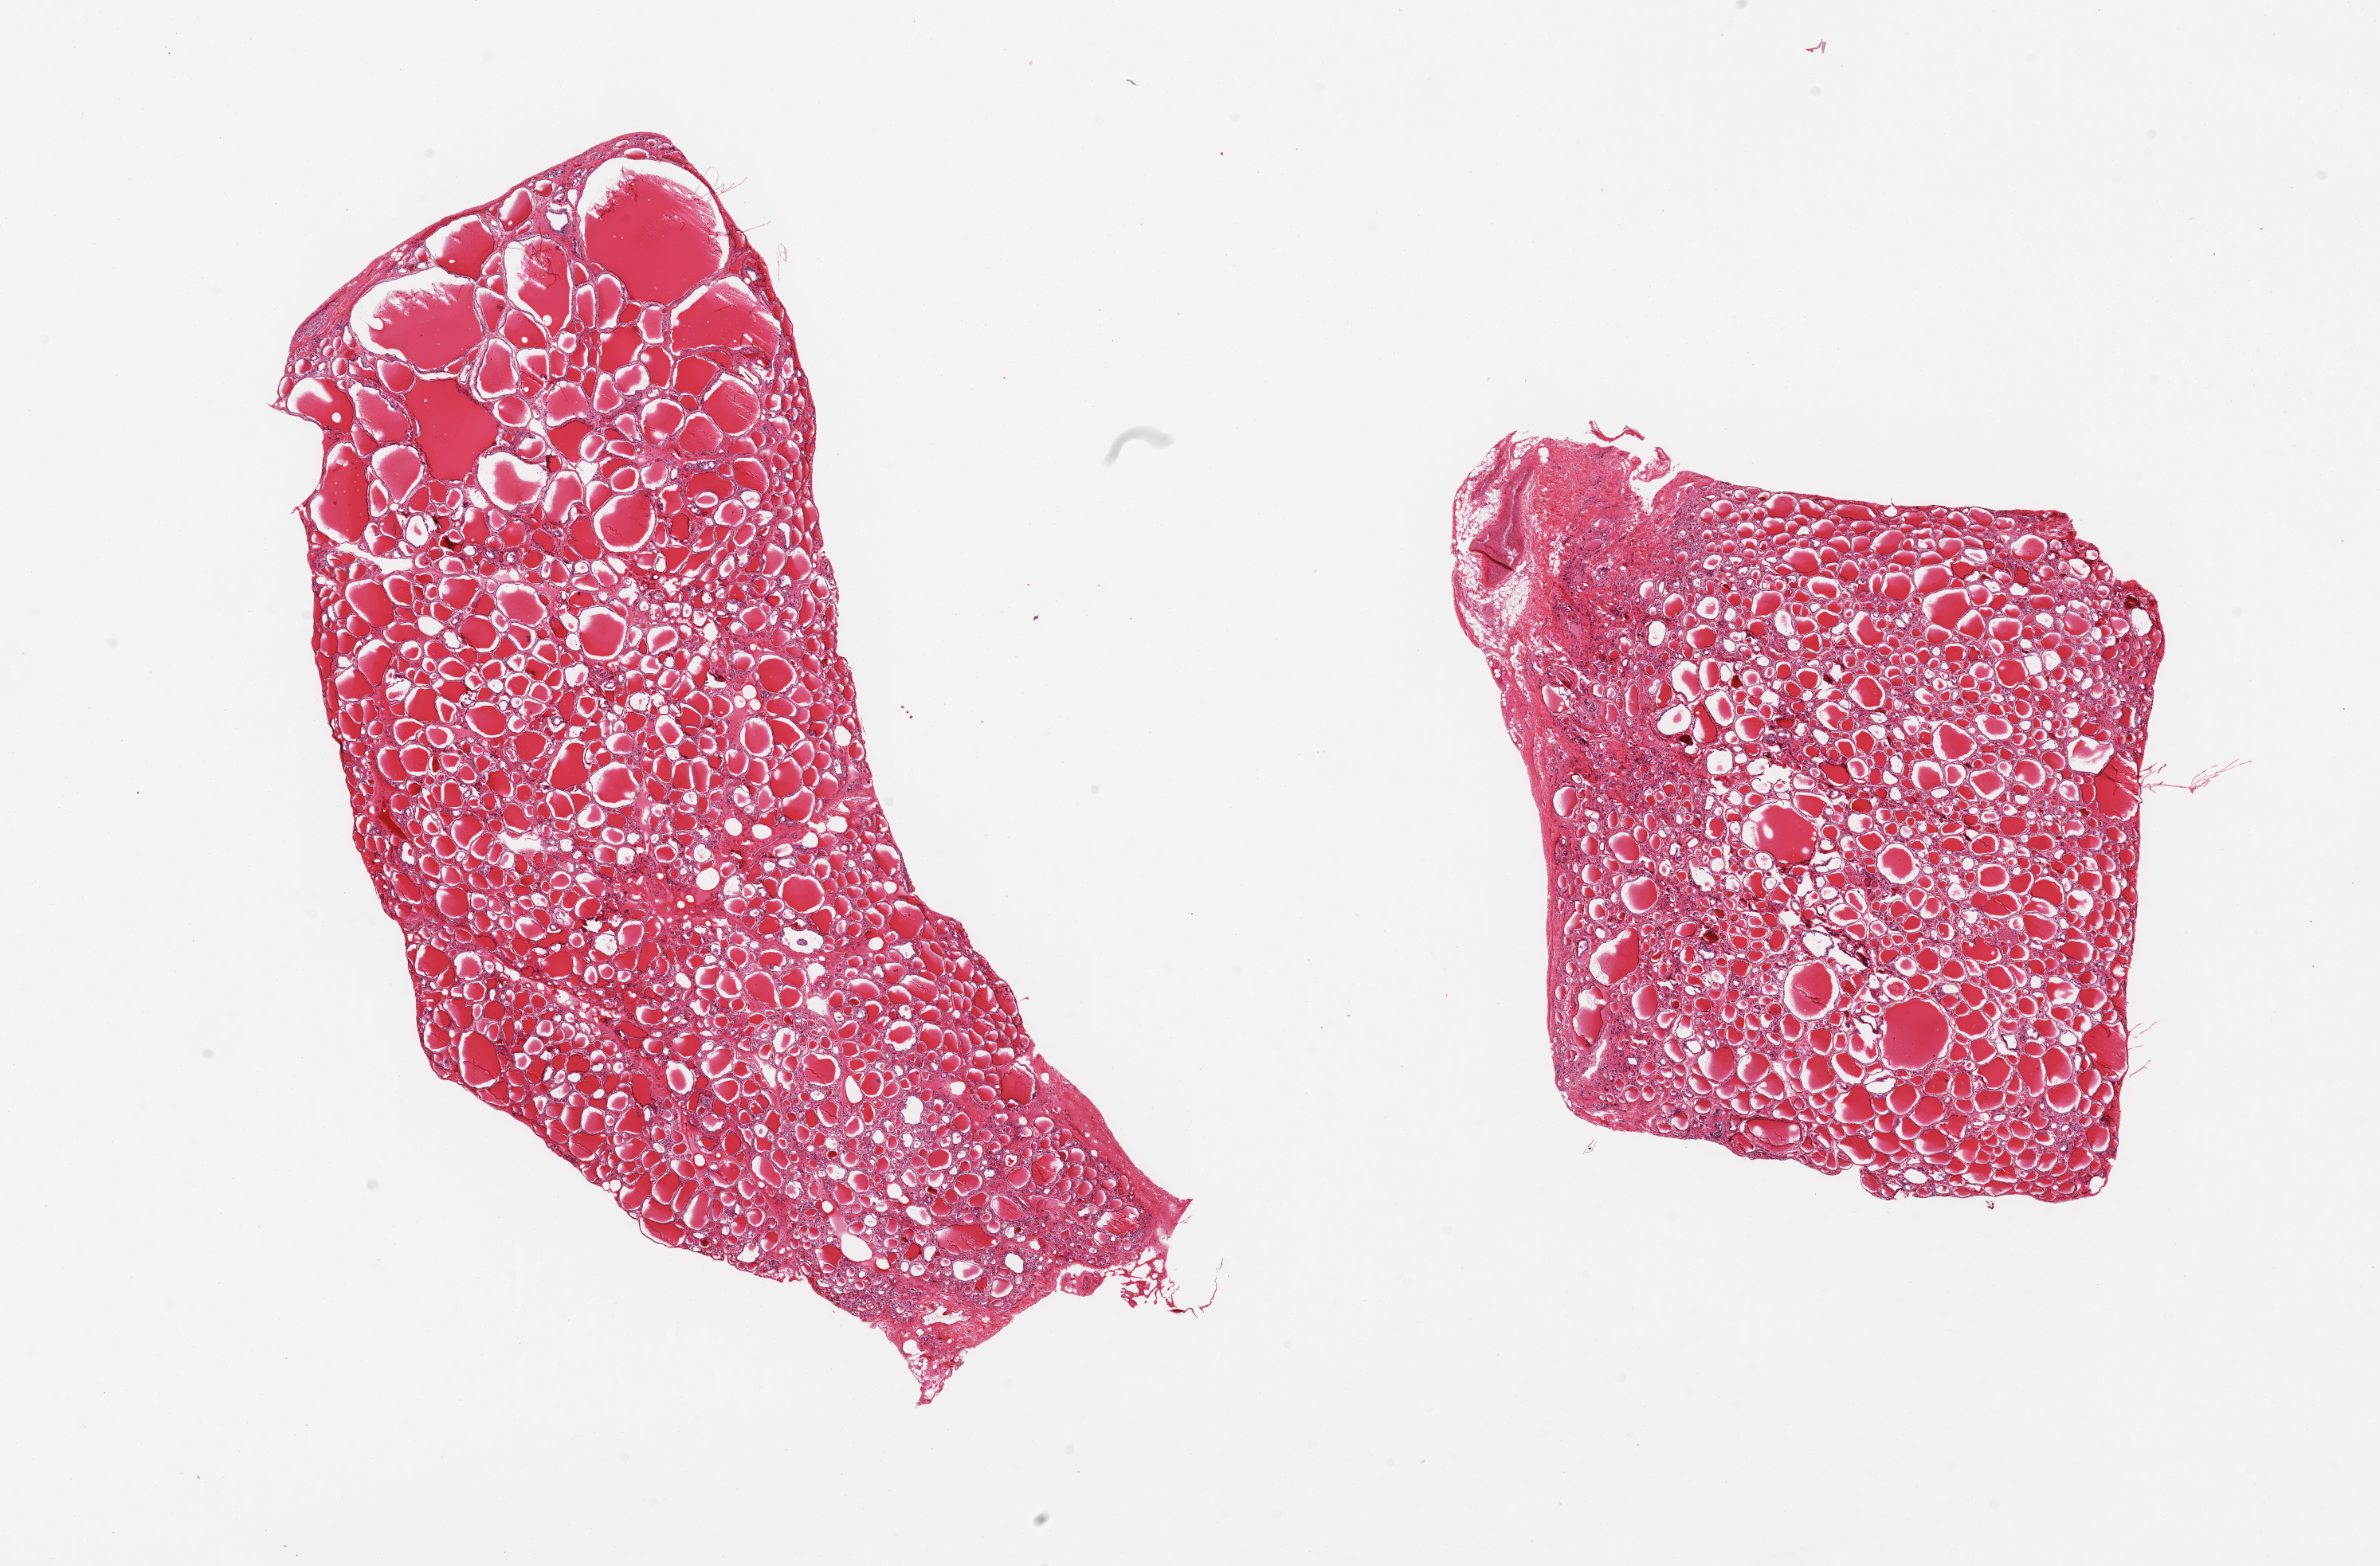
Whole-slide image, haematoxylin and eosin stain, brightfield — low-resolution overview of the scanned area, about 23.6 x 15.6 mm, PAXgene-fixed paraffin-embedded (PFPE) section, sampled site (target tissue): thyroid, tissue donor sample. Donor: male.
* pathologist's review note for this sample: 2 pieces, no abnormalities